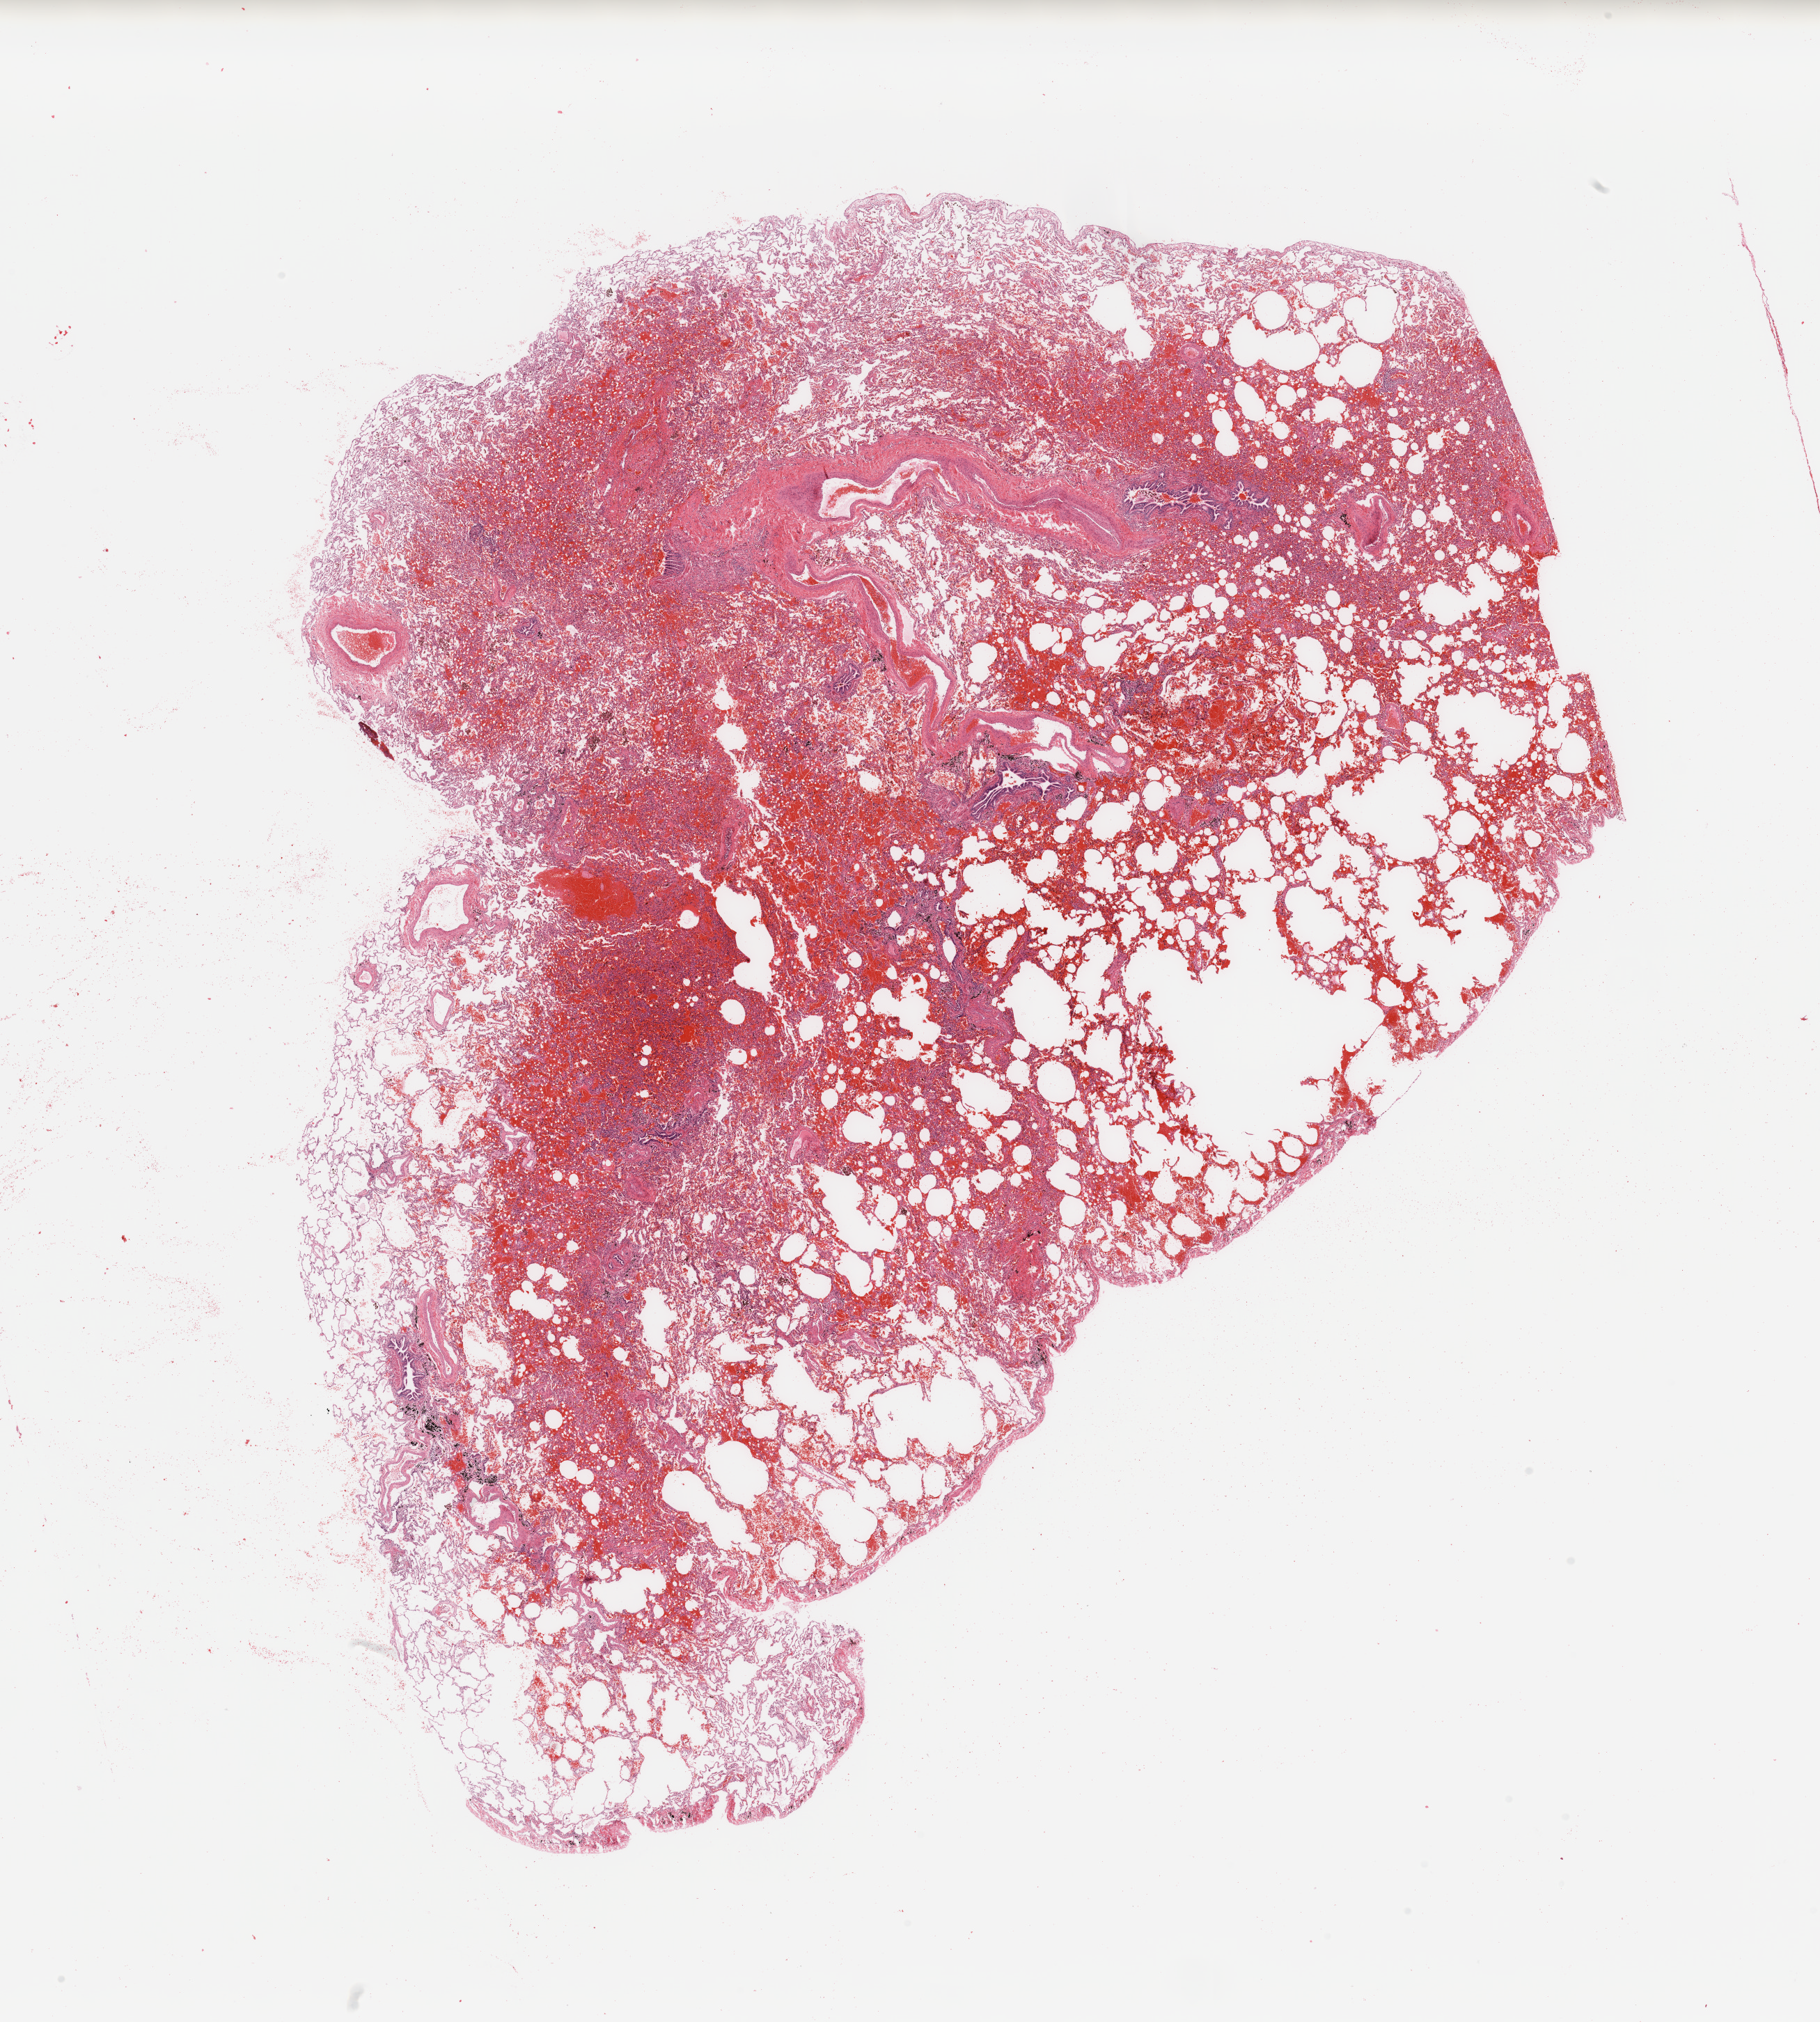
Digitized H&E-stained tissue section (whole slide) — low-resolution overview of the scanned area, about 20.7 x 23.0 mm (slide scanned at 20x), lung, normal (non-tumour) tissue. Male, 60 y/o.
This section: normal (non-tumour) tissue from the same patient. Patient diagnosis: Adenocarcinoma, NOS.